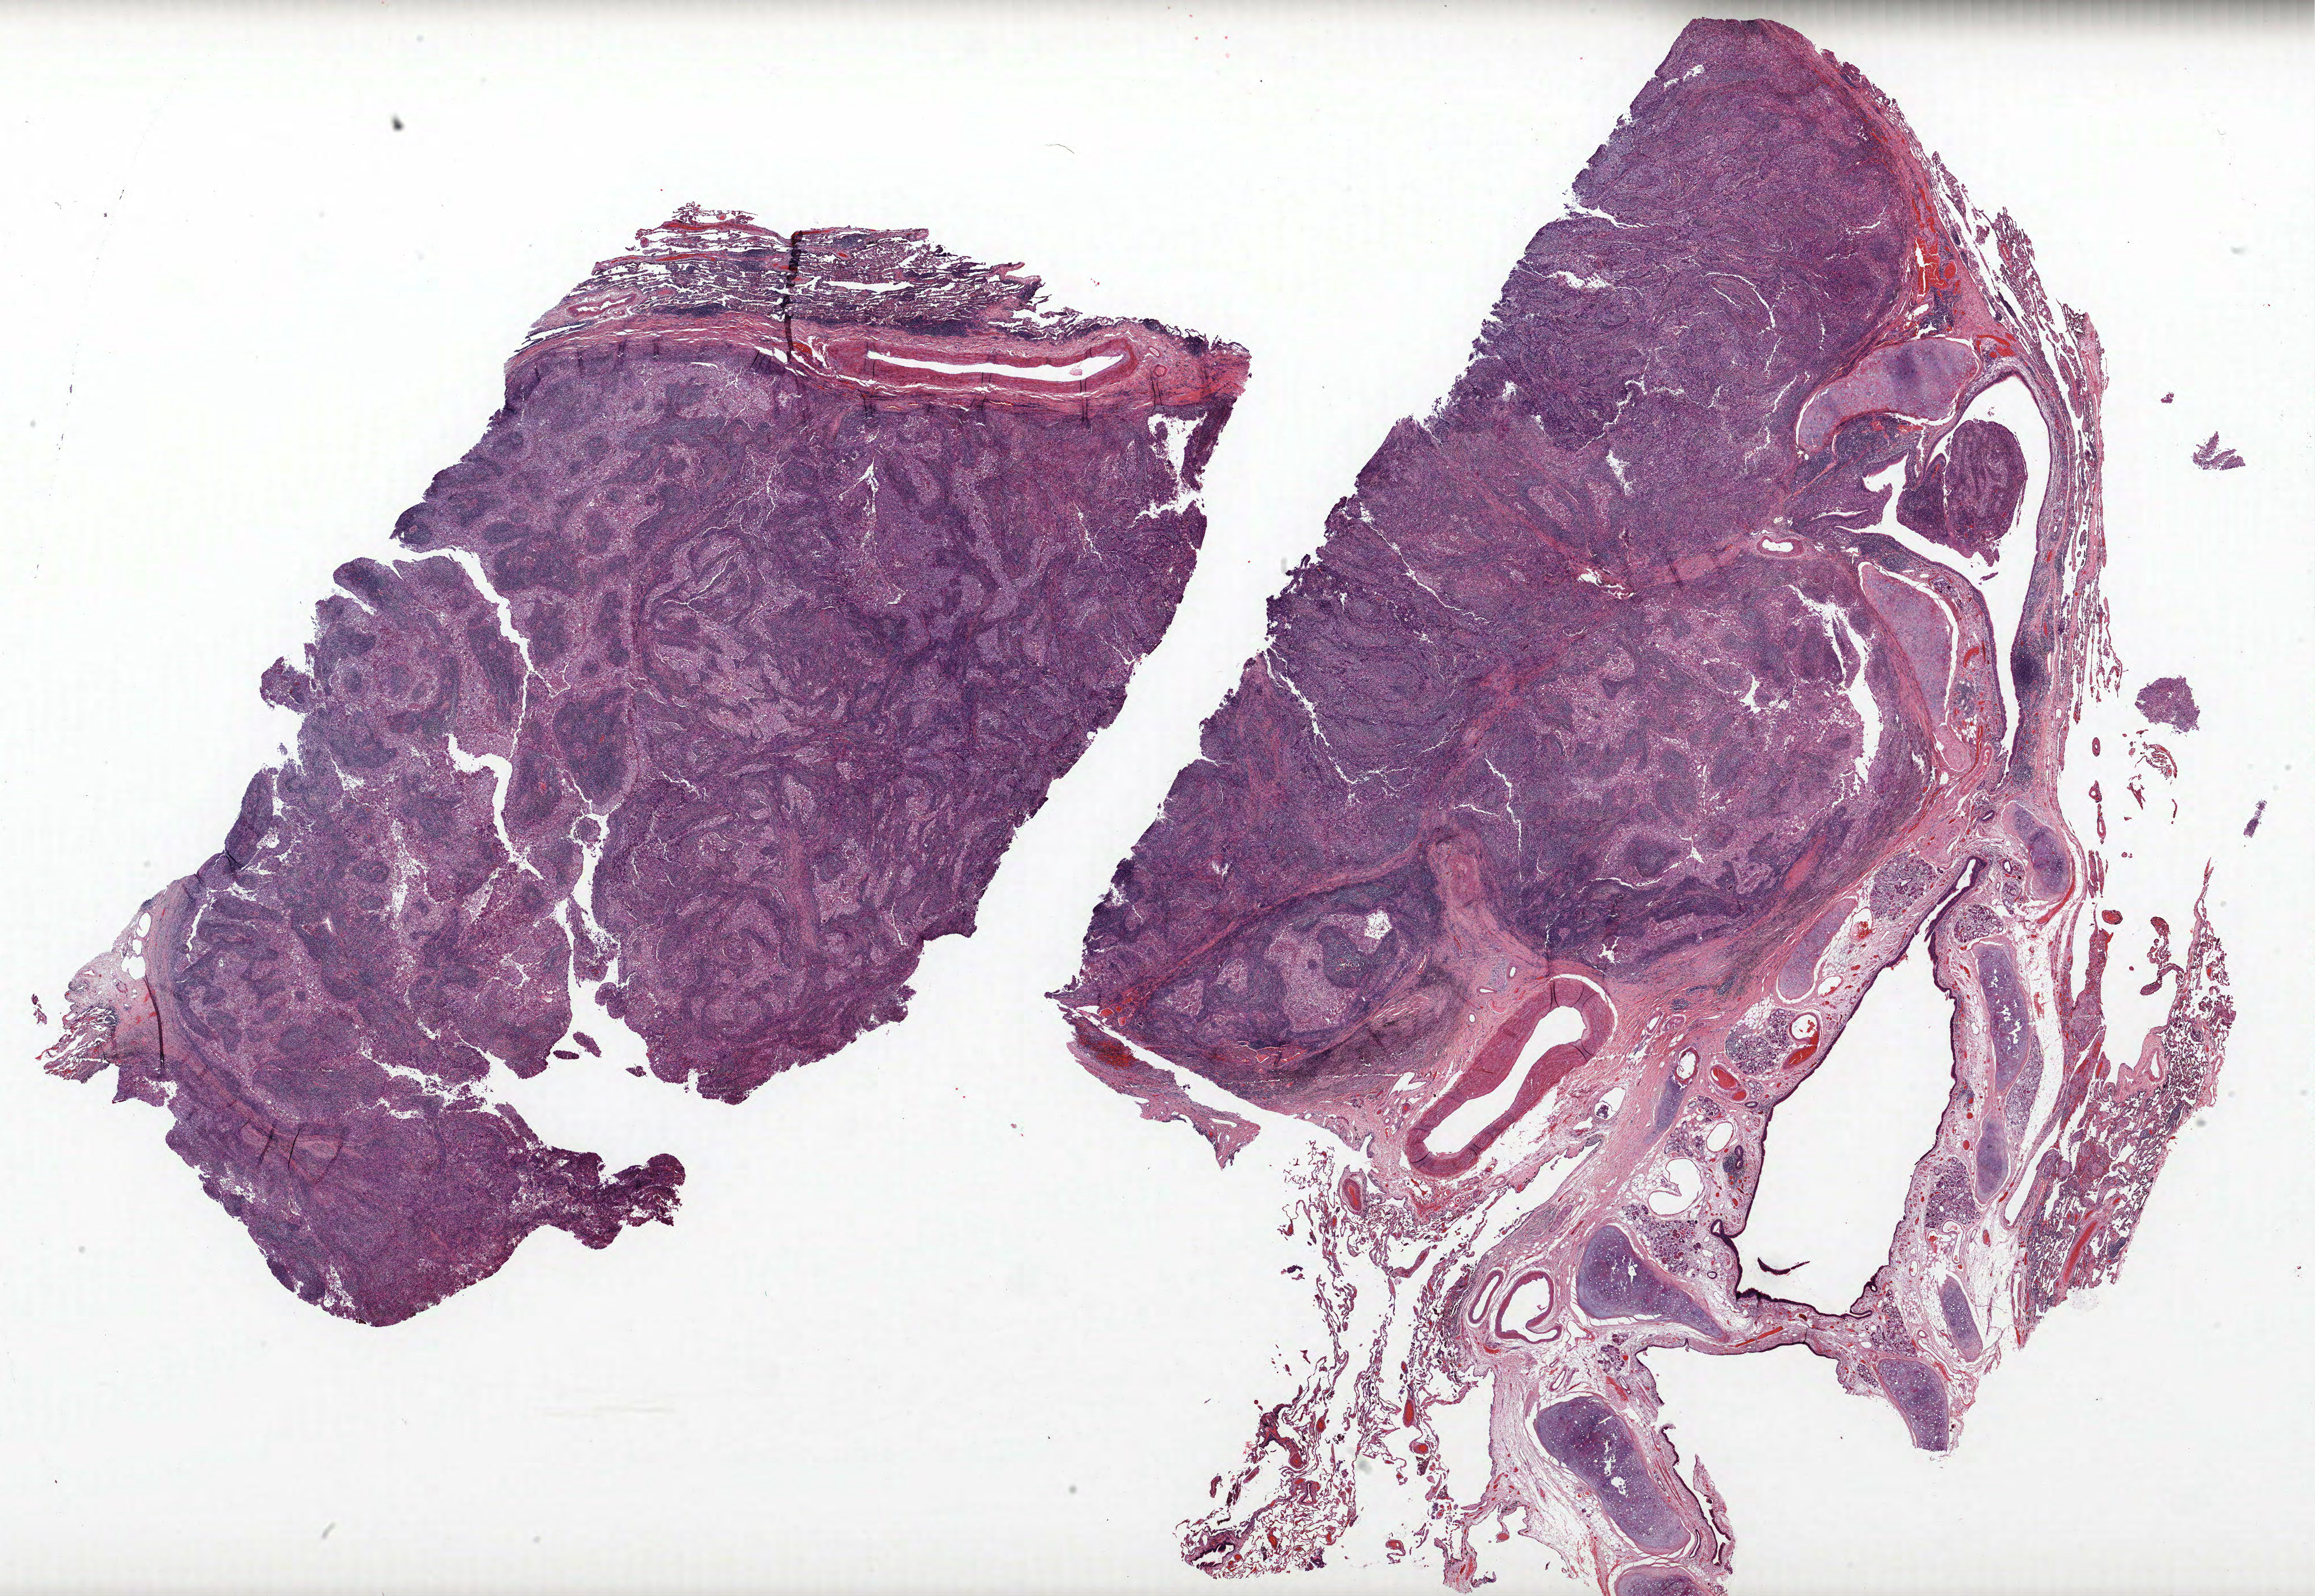
Whole-slide histology image, H&E-stained — whole scanned area (about 32.4 x 22.3 mm, from a 40x scan) shown as a low-resolution overview. Formalin-fixed paraffin-embedded (FFPE) section. Lung. Male patient, aged 70 at enrolment. Former smoker at enrolment. Grade: poorly differentiated (G3).
Tumour size (pathology): 50 mm. Primary tumour location (clinical record): right upper lobe. Participant's lung-cancer diagnosis: Adenocarcinoma, NOS. Stage (AJCC 6th edition): IIIA.